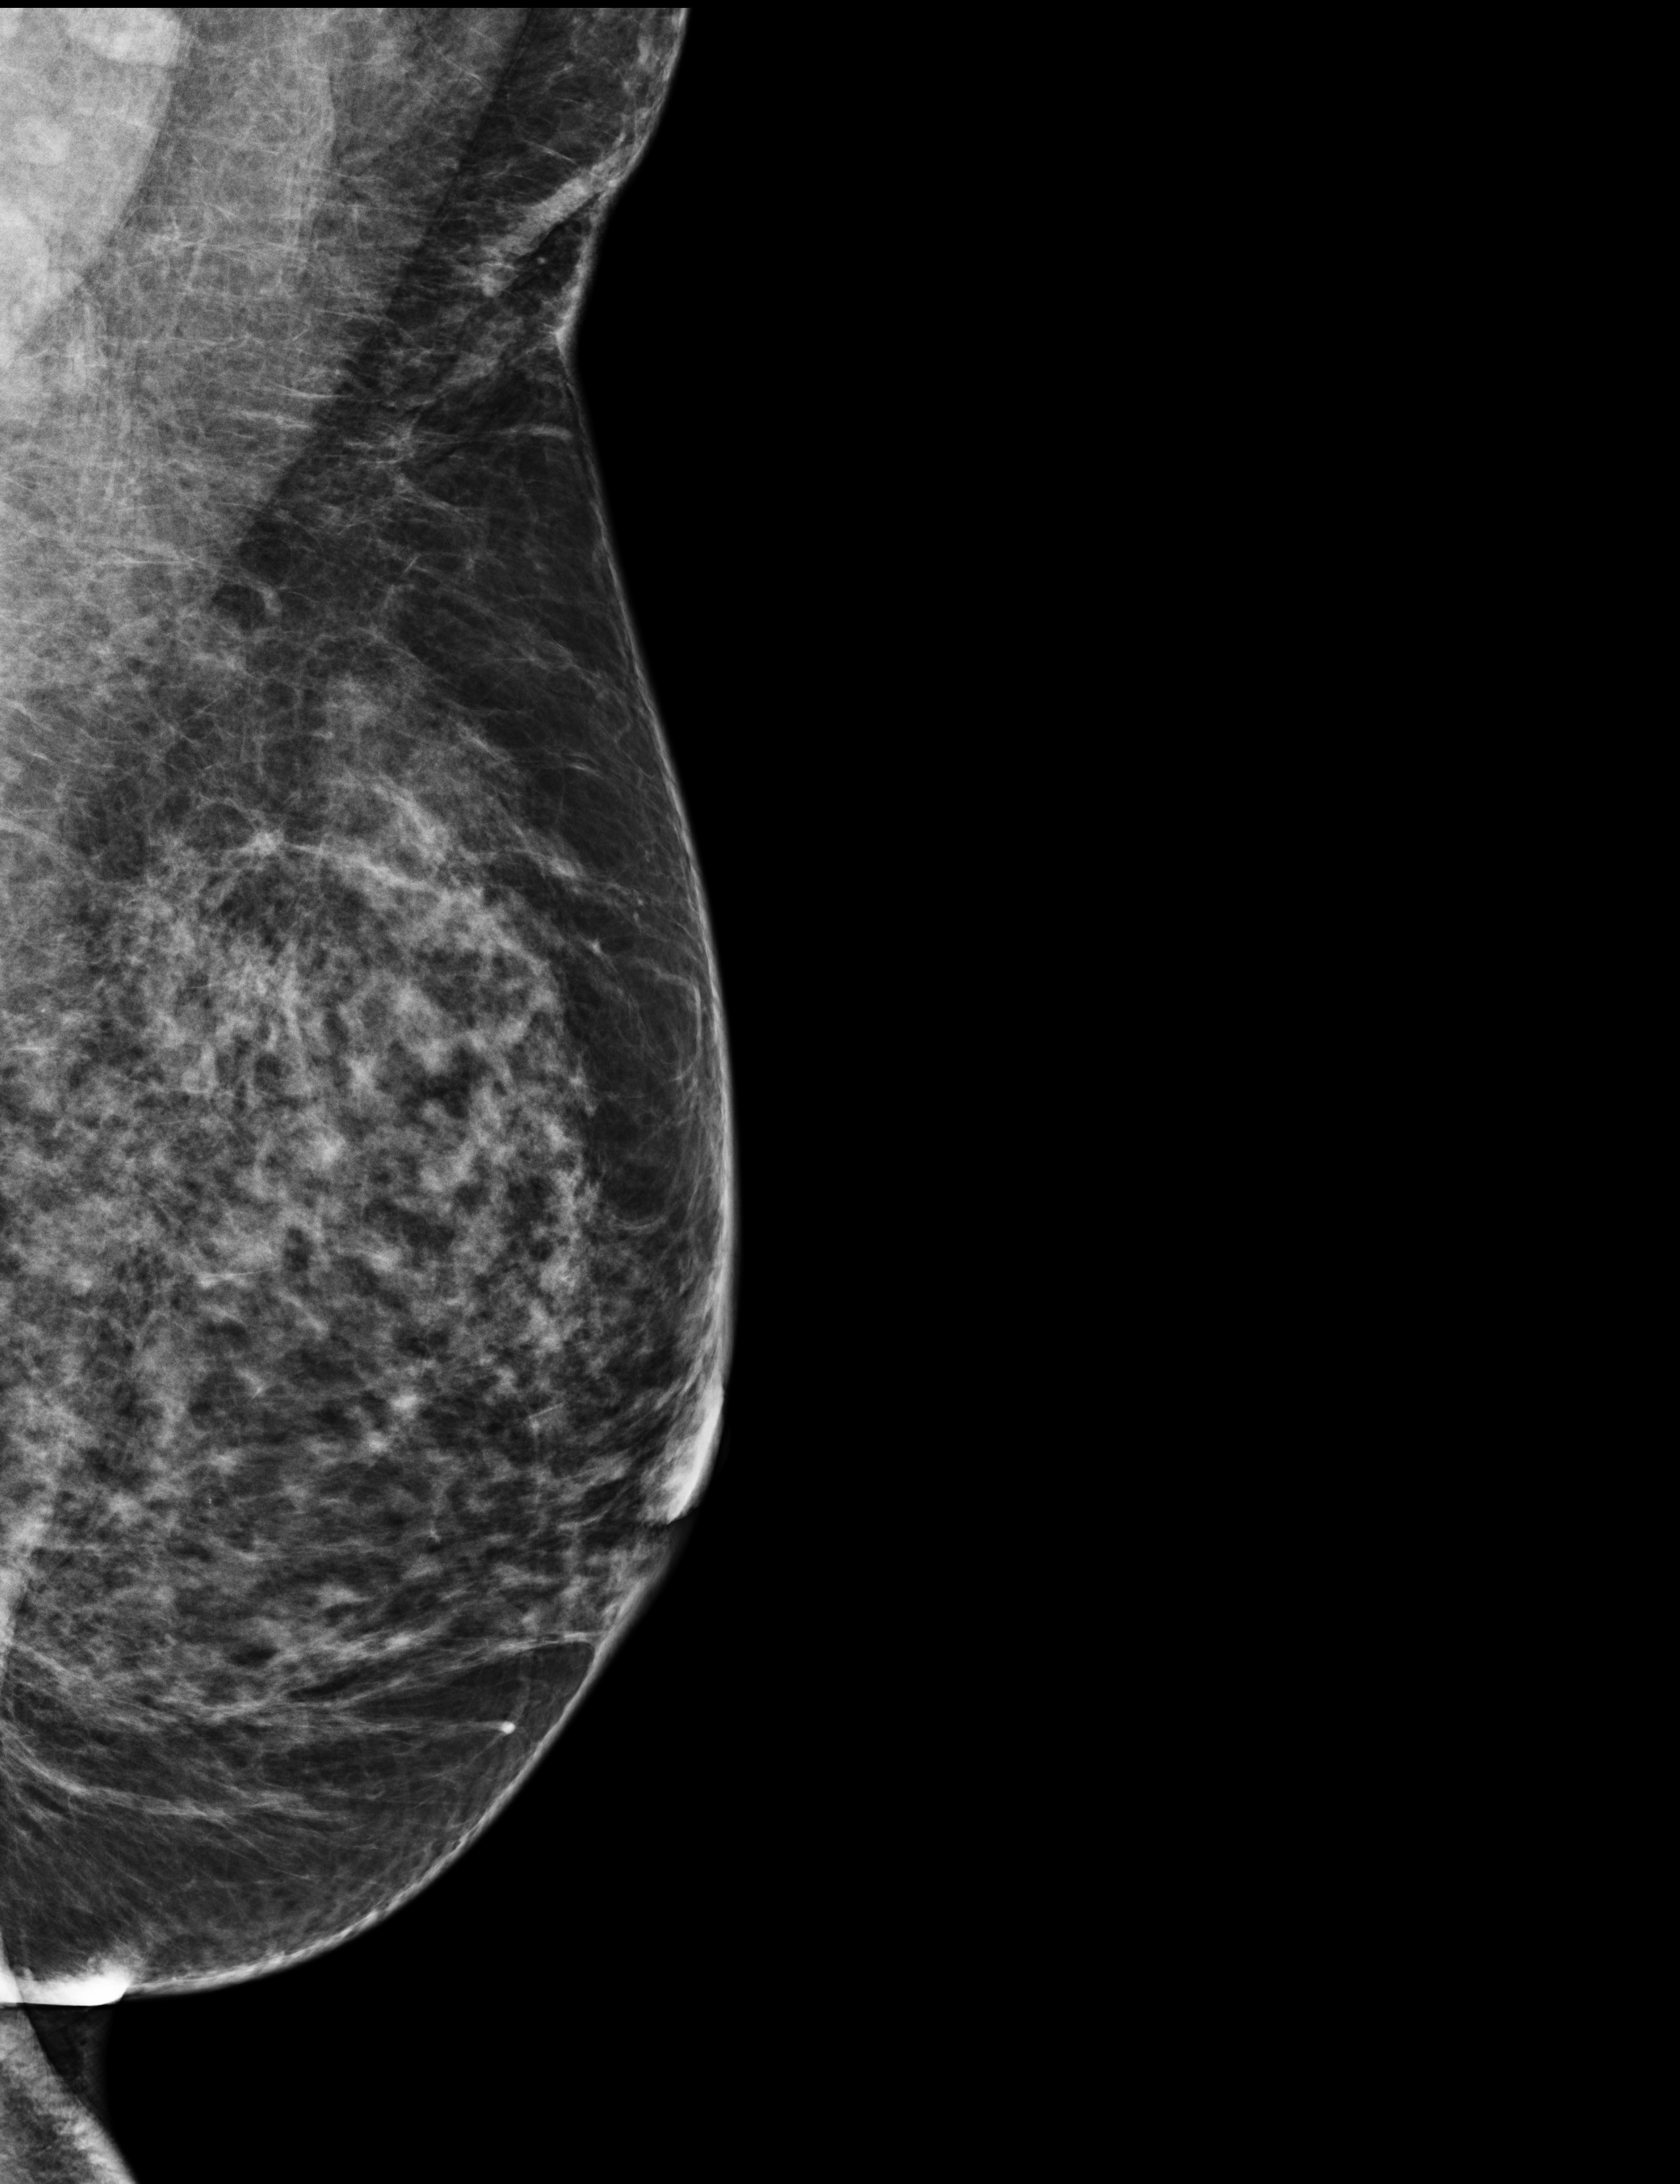
Annual screening mammography examination; compressed breast thickness 68 mm; system: Selenia Dimensions. Patient: female, 53 years.
Image type: full-field digital mammogram. Breast: left. Projection: mediolateral oblique (MLO) view.